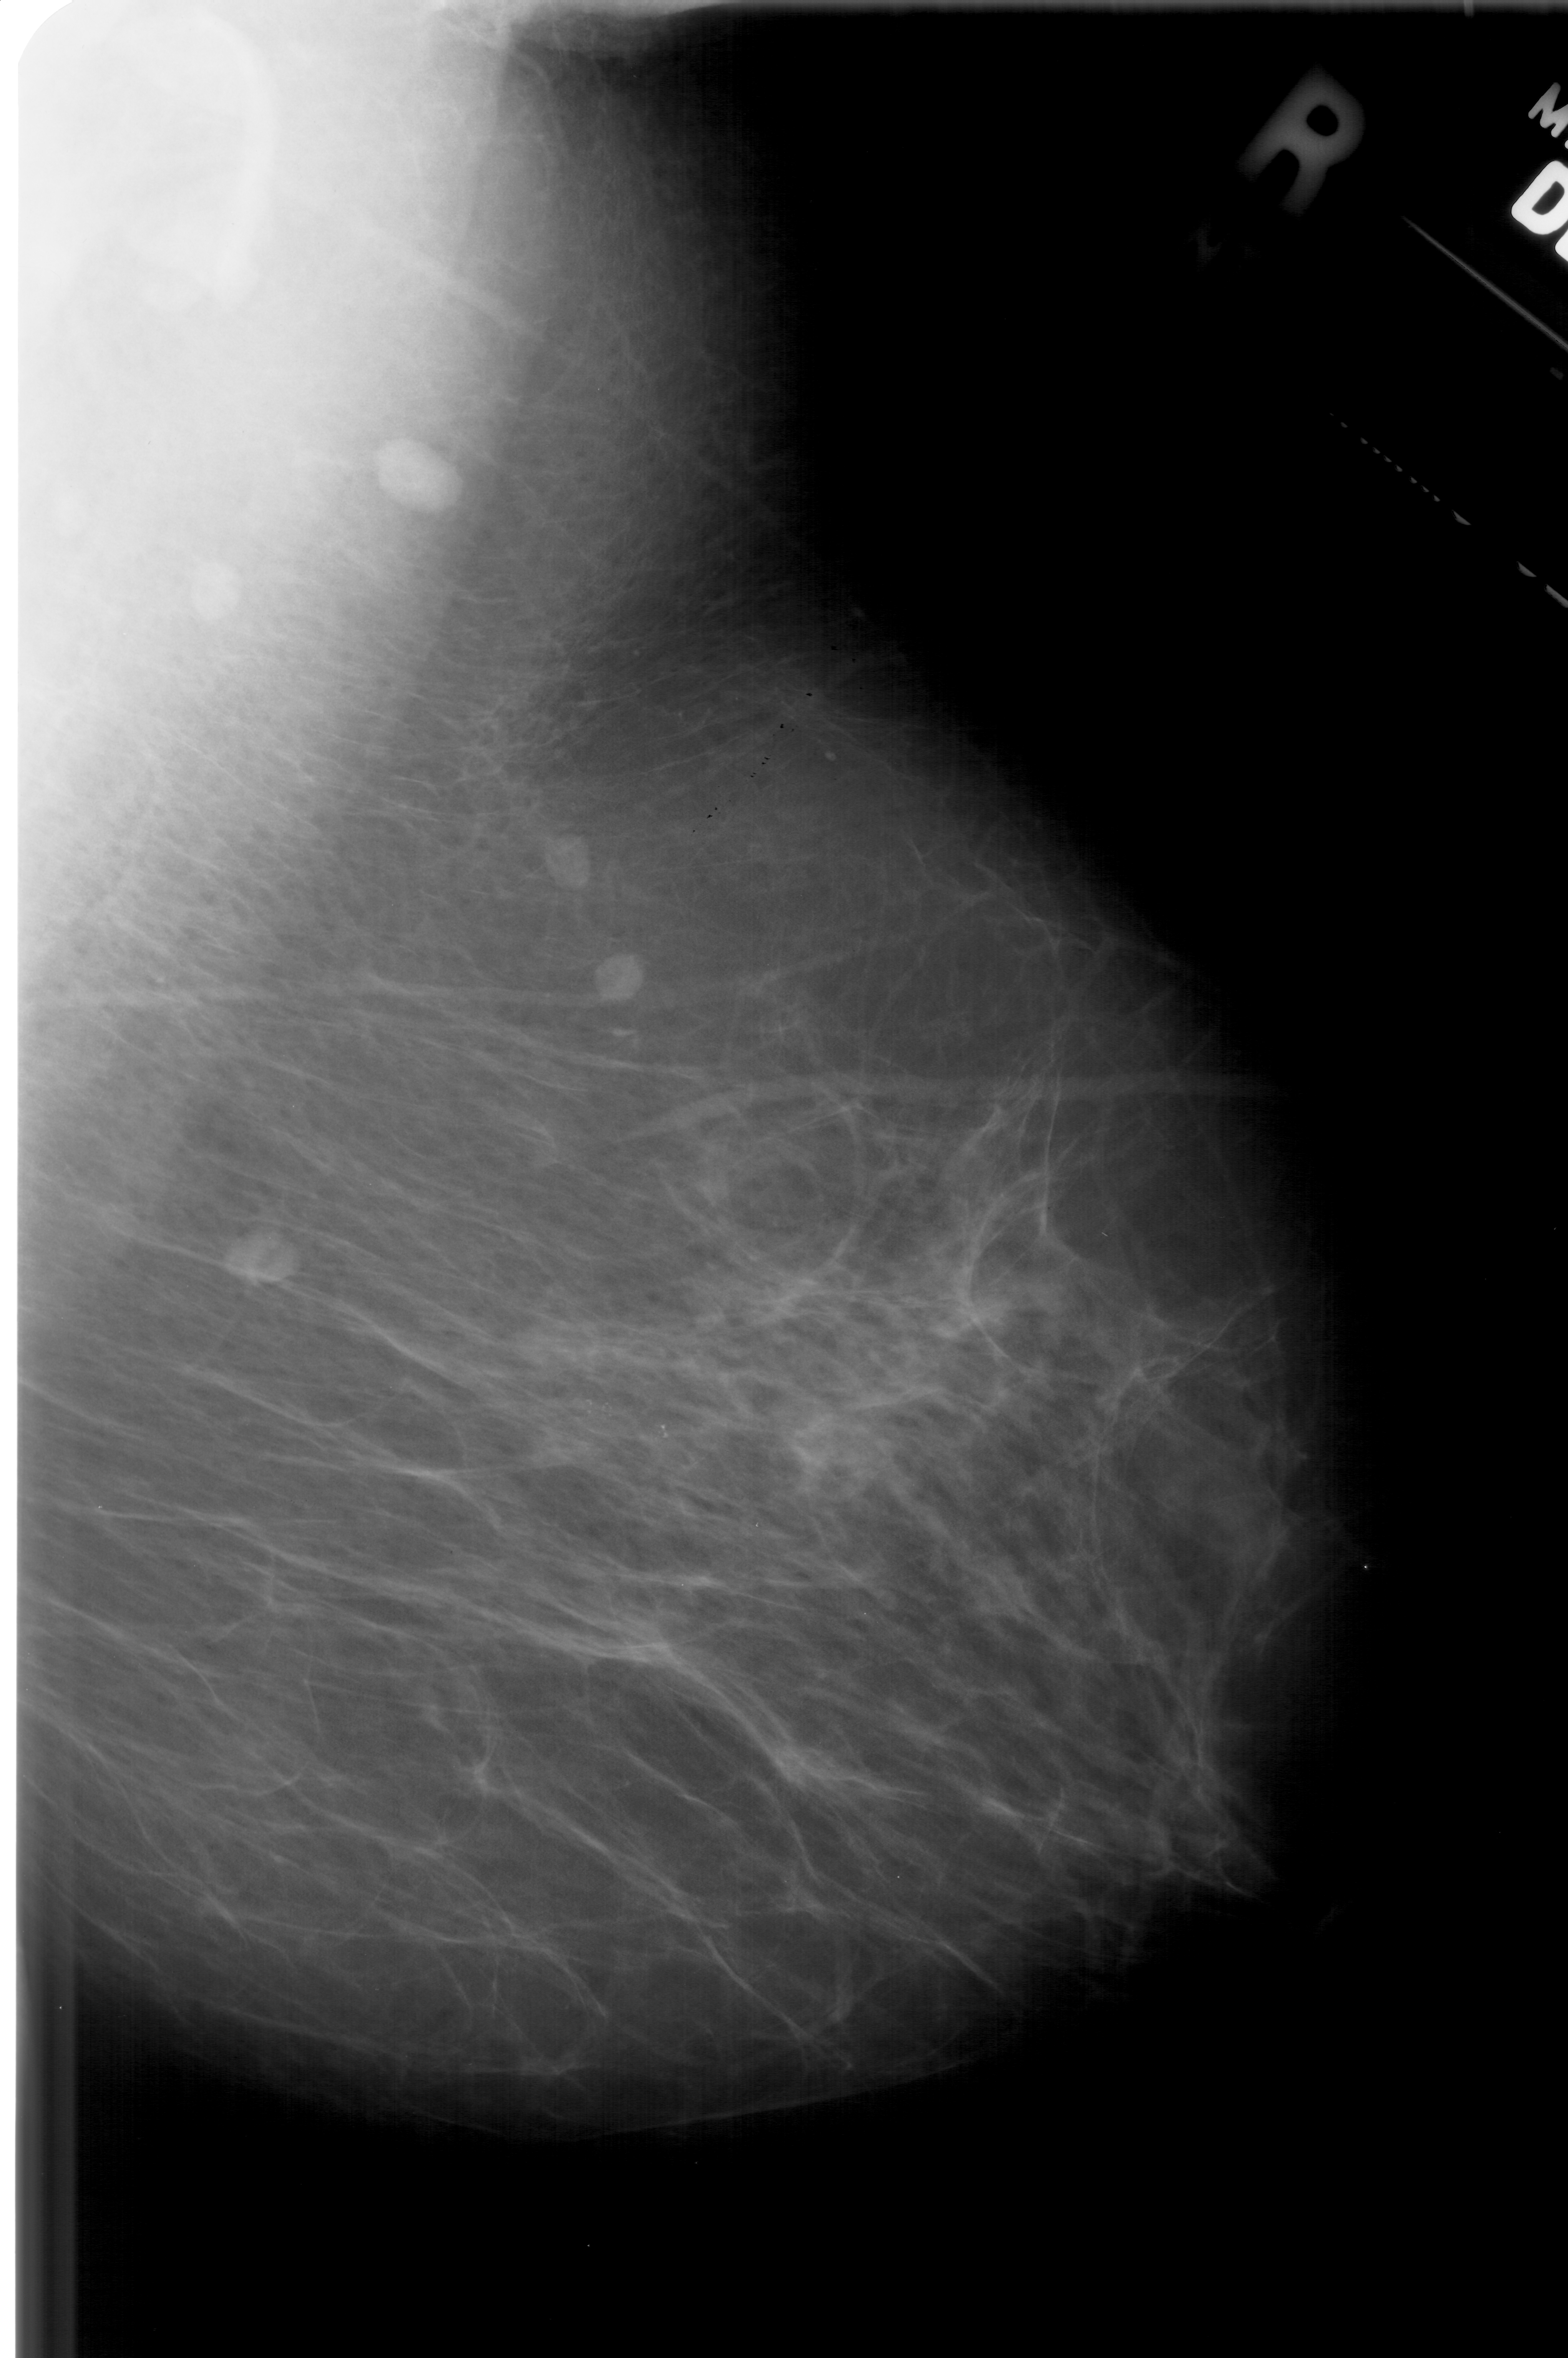
Scanned film-screen mammogram. Right breast. Mediolateral oblique (MLO) view. BI-RADS breast density category 2 (scale 1–4). 1568 × 2358 image matrix.
Expert-marked regions of interest on this film, with their recorded descriptors:
- calcifications, morphology pleomorphic, distribution clustered; BI-RADS assessment category 4; subtlety rating 3 on a 1 (subtle) to 5 (obvious) scale; pathology (as recorded): benign: bounding box [x1, y1, x2, y2] px = [560, 1397, 669, 1460]